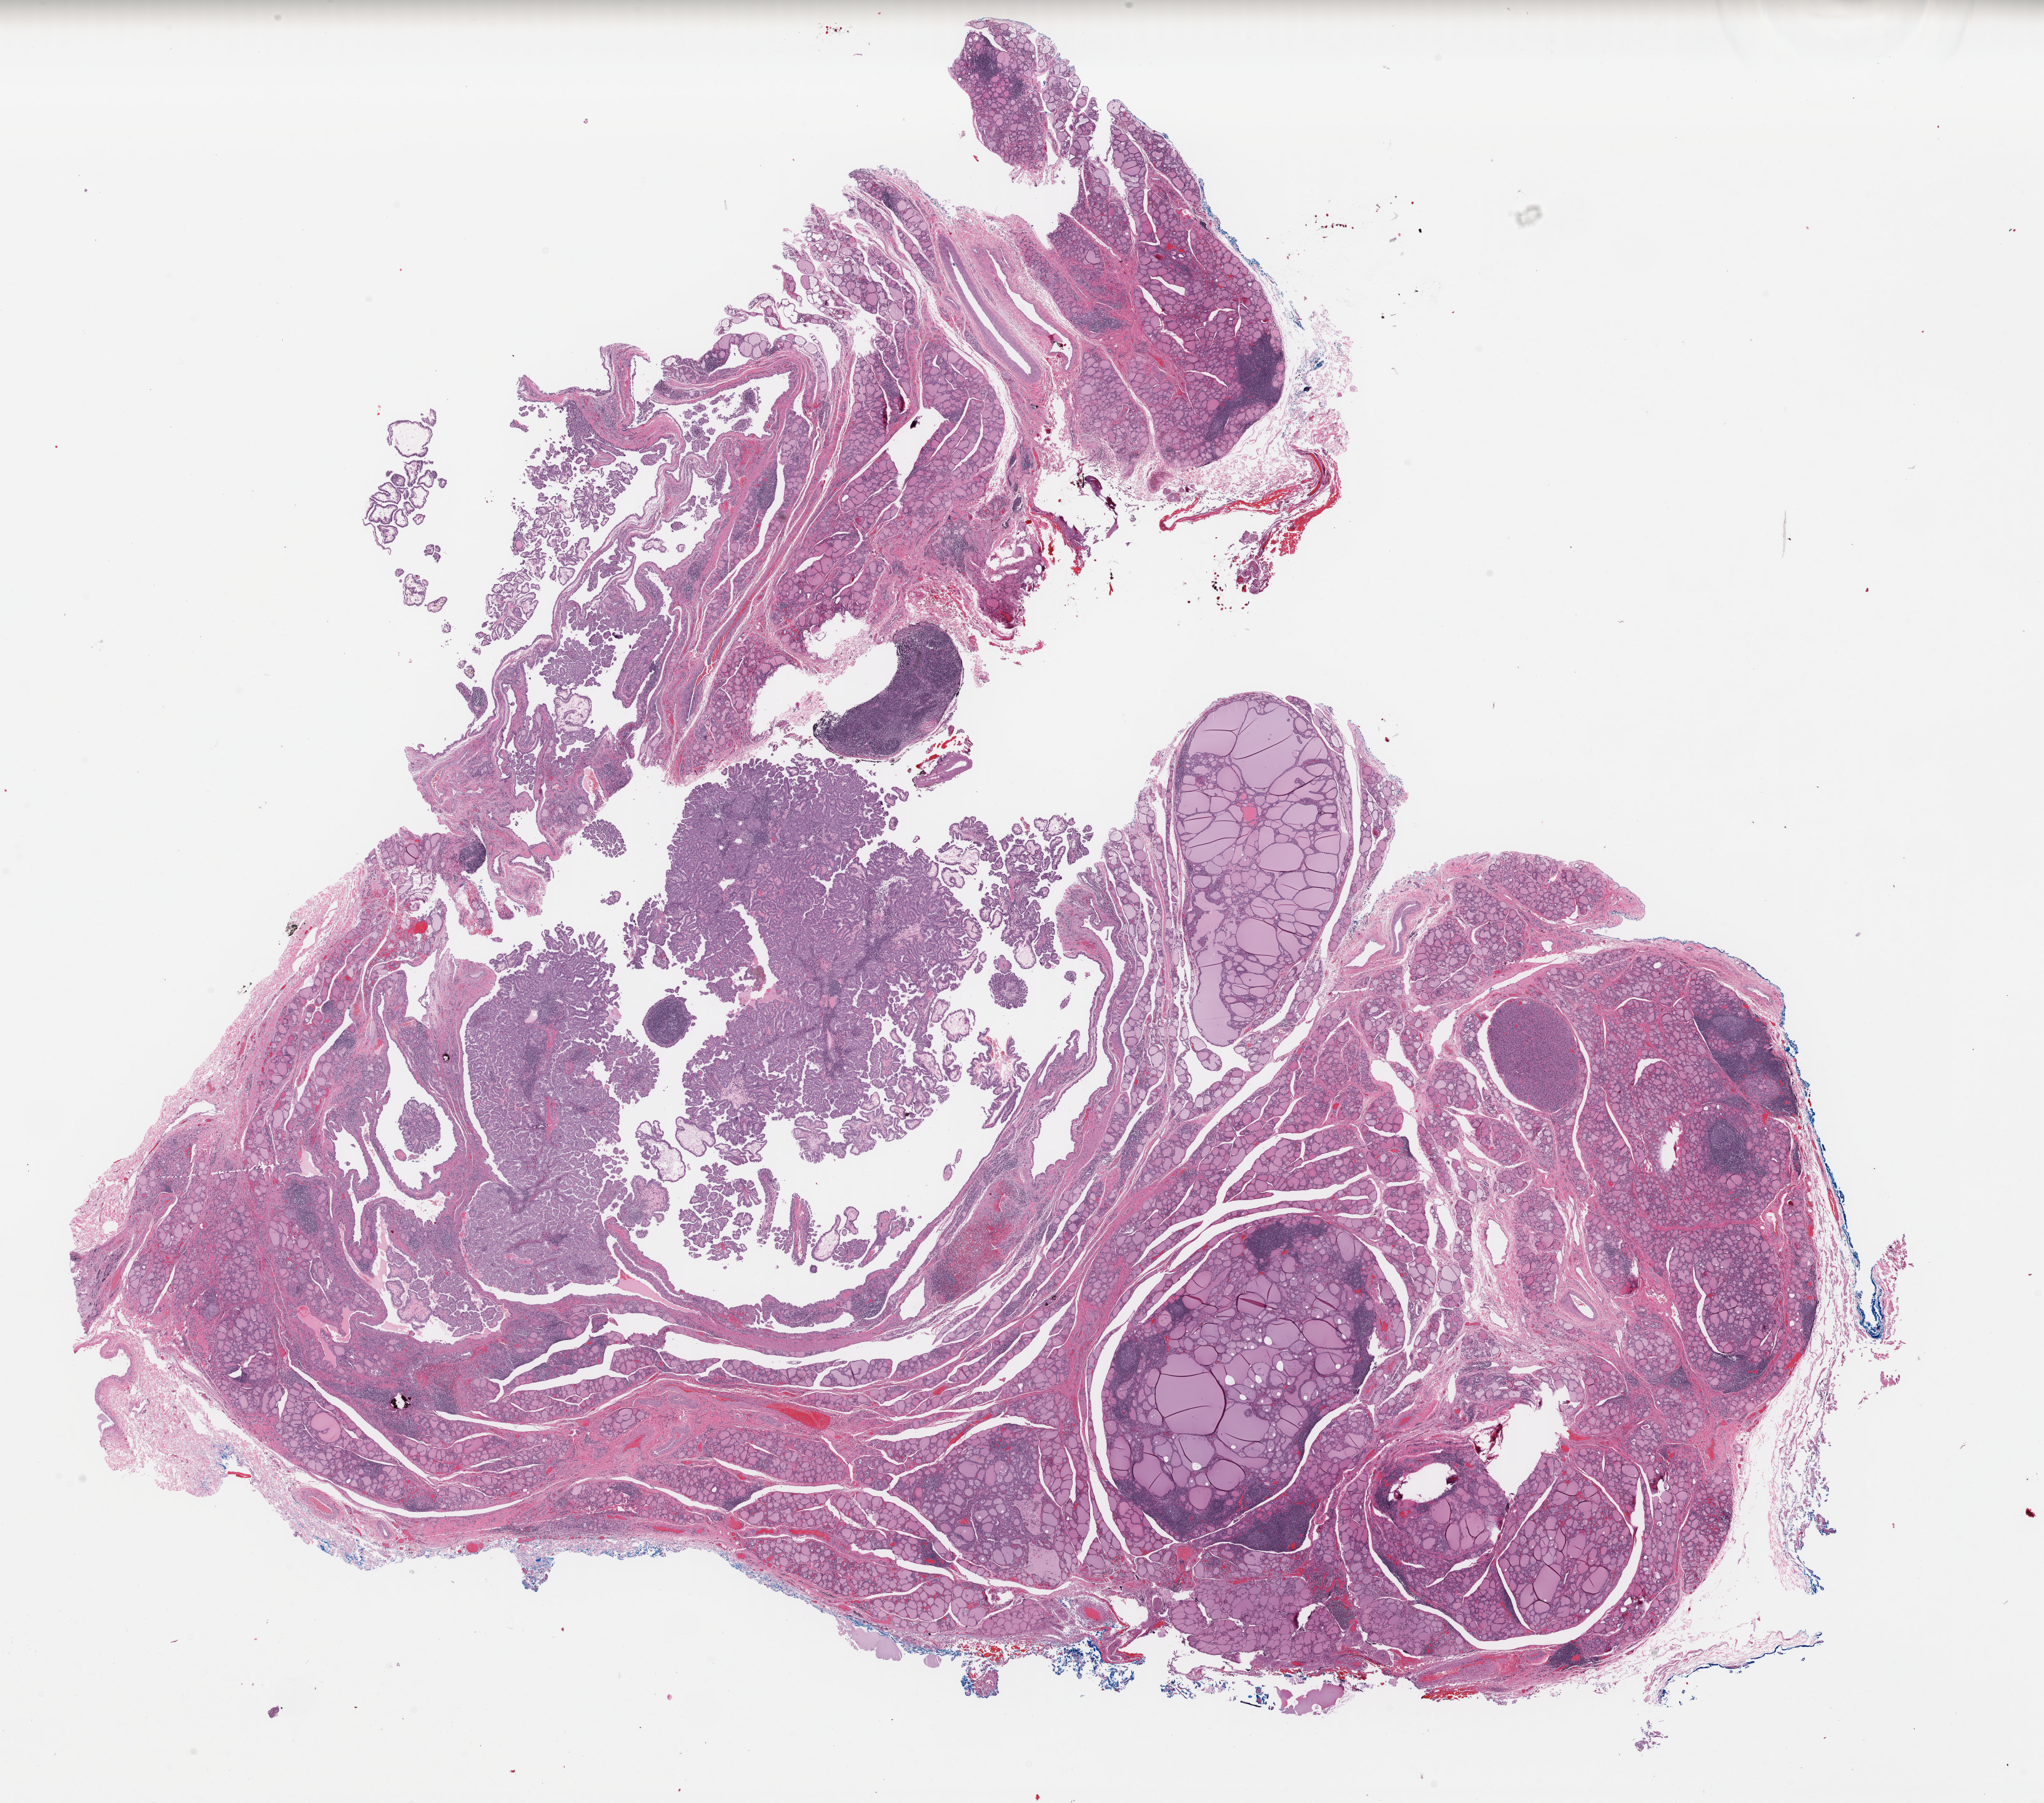
Digitized Hematoxylin and eosin (H&E) stained tissue section (whole slide) — low-resolution overview of the scanned area, about 25.8 x 22.8 mm (slide scanned at 40x); FFPE section; primary tumour sample from the thyroid. Female patient; age at initial diagnosis 52 years.
Histologic diagnosis: Papillary adenocarcinoma, NOS (thyroid gland). AJCC pathologic stage: III (7th edition). Lymph nodes positive (case pathology): 3 of 5 examined.